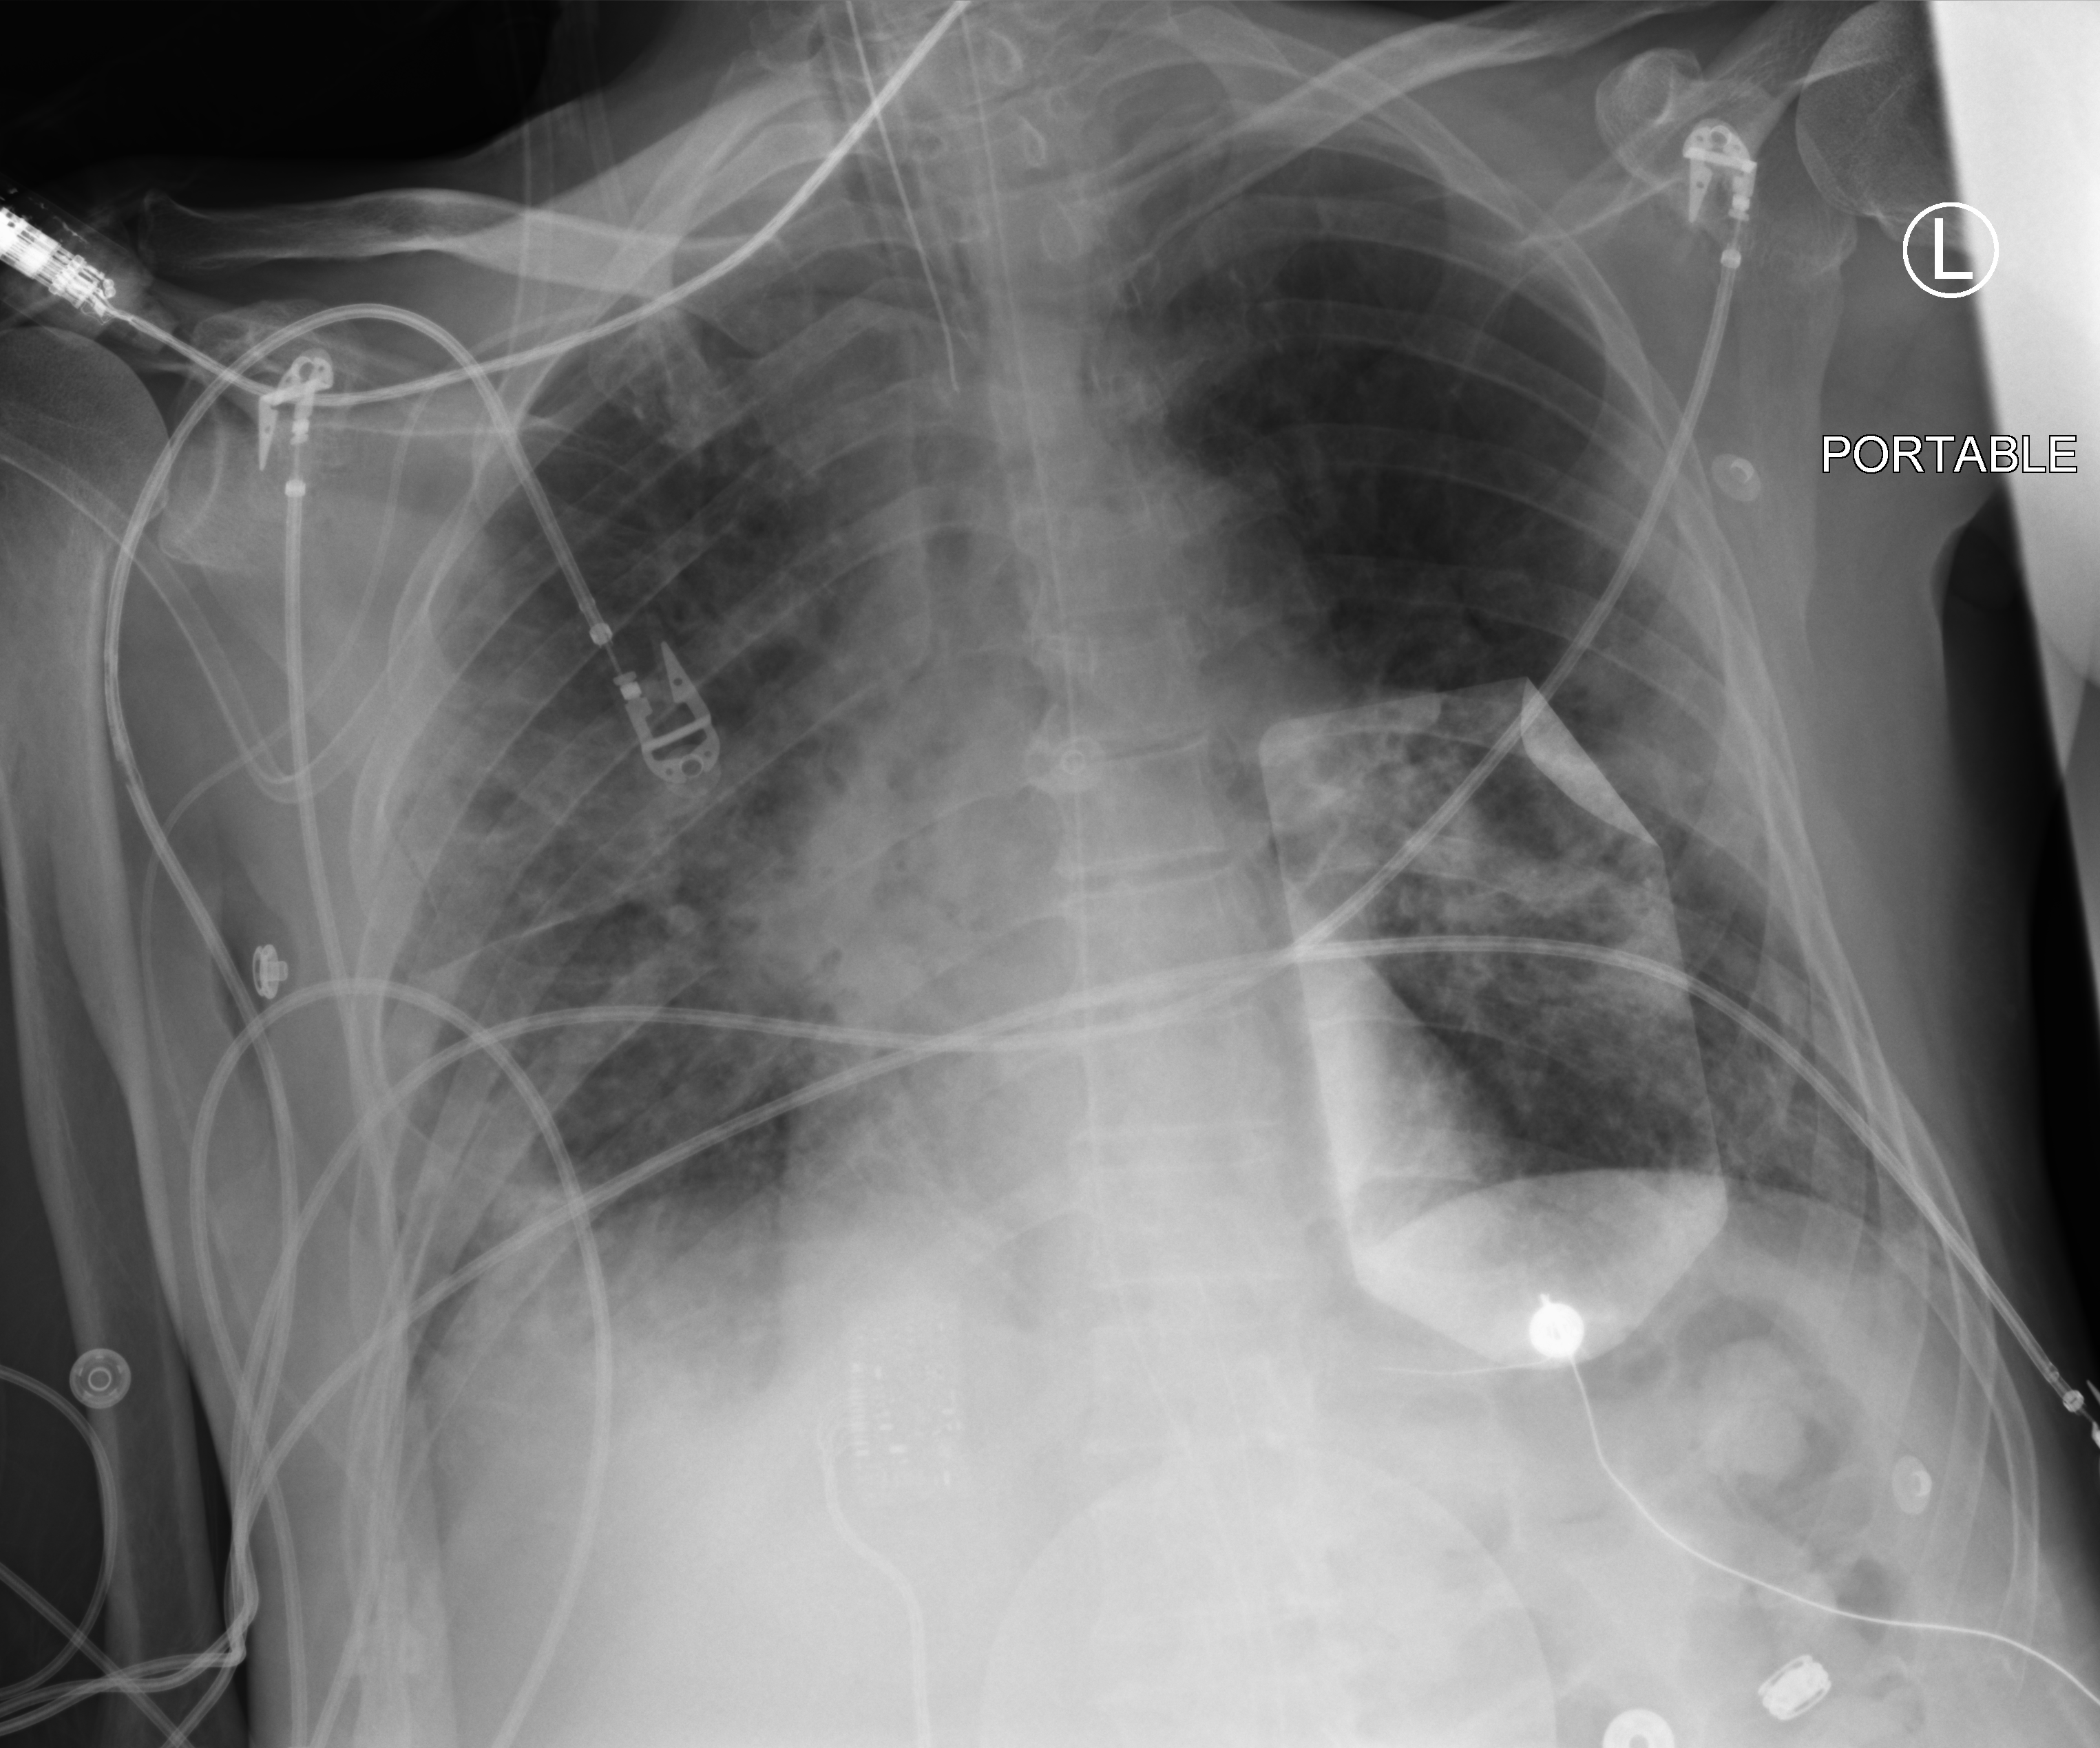
Chest X-ray (portable). Male patient hospitalised with COVID-19, age 75–90 years.
From the hospital-stay record, not from the radiograph (when in the stay this image was taken is not recorded): smoking status (admission record): never; mechanically ventilated during this hospital stay: yes.